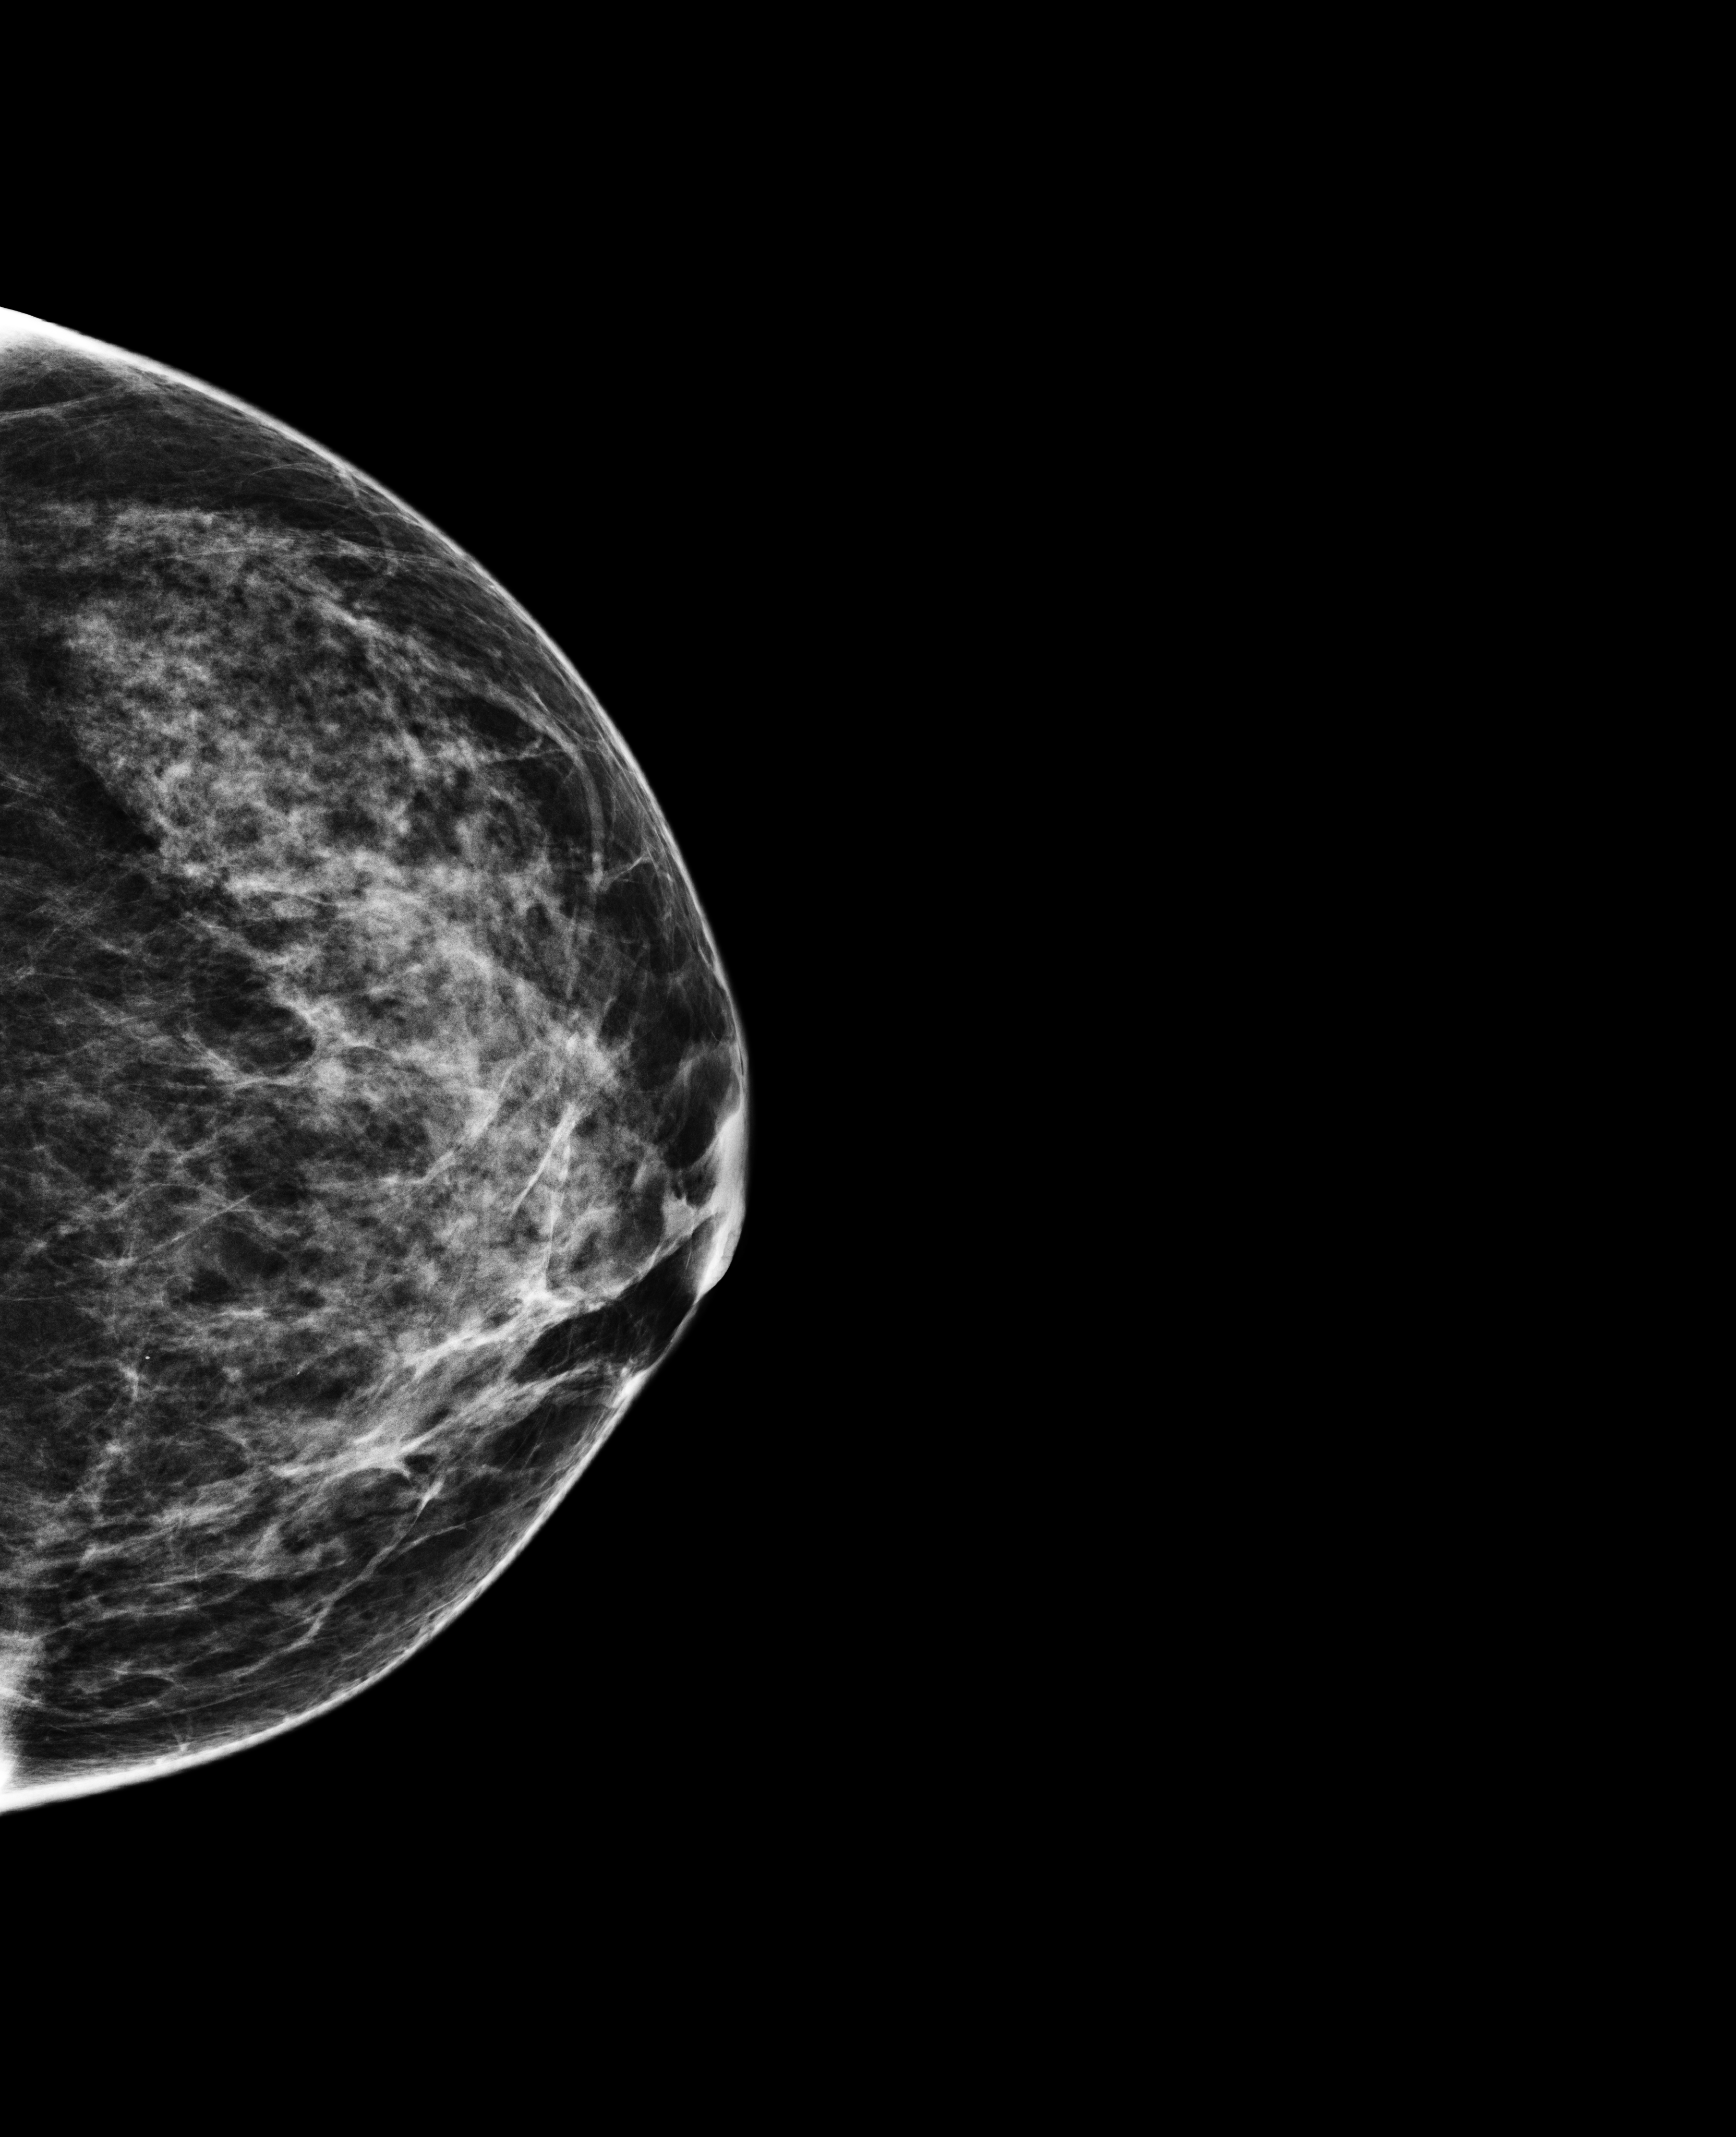
Full-field digital mammogram (FFDM), left breast, craniocaudal (CC) view, annual screening mammography examination, compressed breast thickness 50 mm, system: Selenia Dimensions. Patient: female, 46 years.
BI-RADS breast density category at the screening exam (both breasts, scale 1–4): 3. Final BI-RADS assessment for this screening round (tomosynthesis exam, both breasts): category 1. Recall: no recall after this screen.